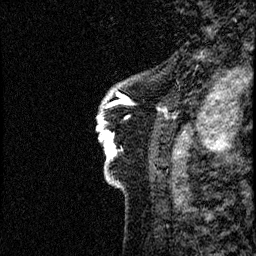
Breast MRI (dynamic contrast-enhanced), one sagittal slice. Position 6 of 60 along the scan axis. Dynamic contrast-enhanced study with each time point stored as its own series, time point 2 of 4 at this slice position (early post-contrast, ordered by acquisition time). 1.5 T. TE 4.2 ms, TR 17.6 ms. 2 mm slice thickness. 256 × 256 image matrix, field of view 200 × 200 mm. Patient: female, 40 years. From the clinical record (not read from this slice): setting: breast cancer imaged before/during neoadjuvant chemotherapy; receptor status: HER2-positive.
Structures marked on this image (semi-automatic segmentation, software-assisted and operator-edited):
- analysis volume of interest (the breast-tissue region the enhancement analysis was run in; not a lesion): bounding box (x1, y1, x2, y2) in pixels: (94, 59, 185, 206)
- tumour enhancement mask (voxels above the 100 % enhancement threshold inside the analysis volume of interest): (96, 91, 161, 169)